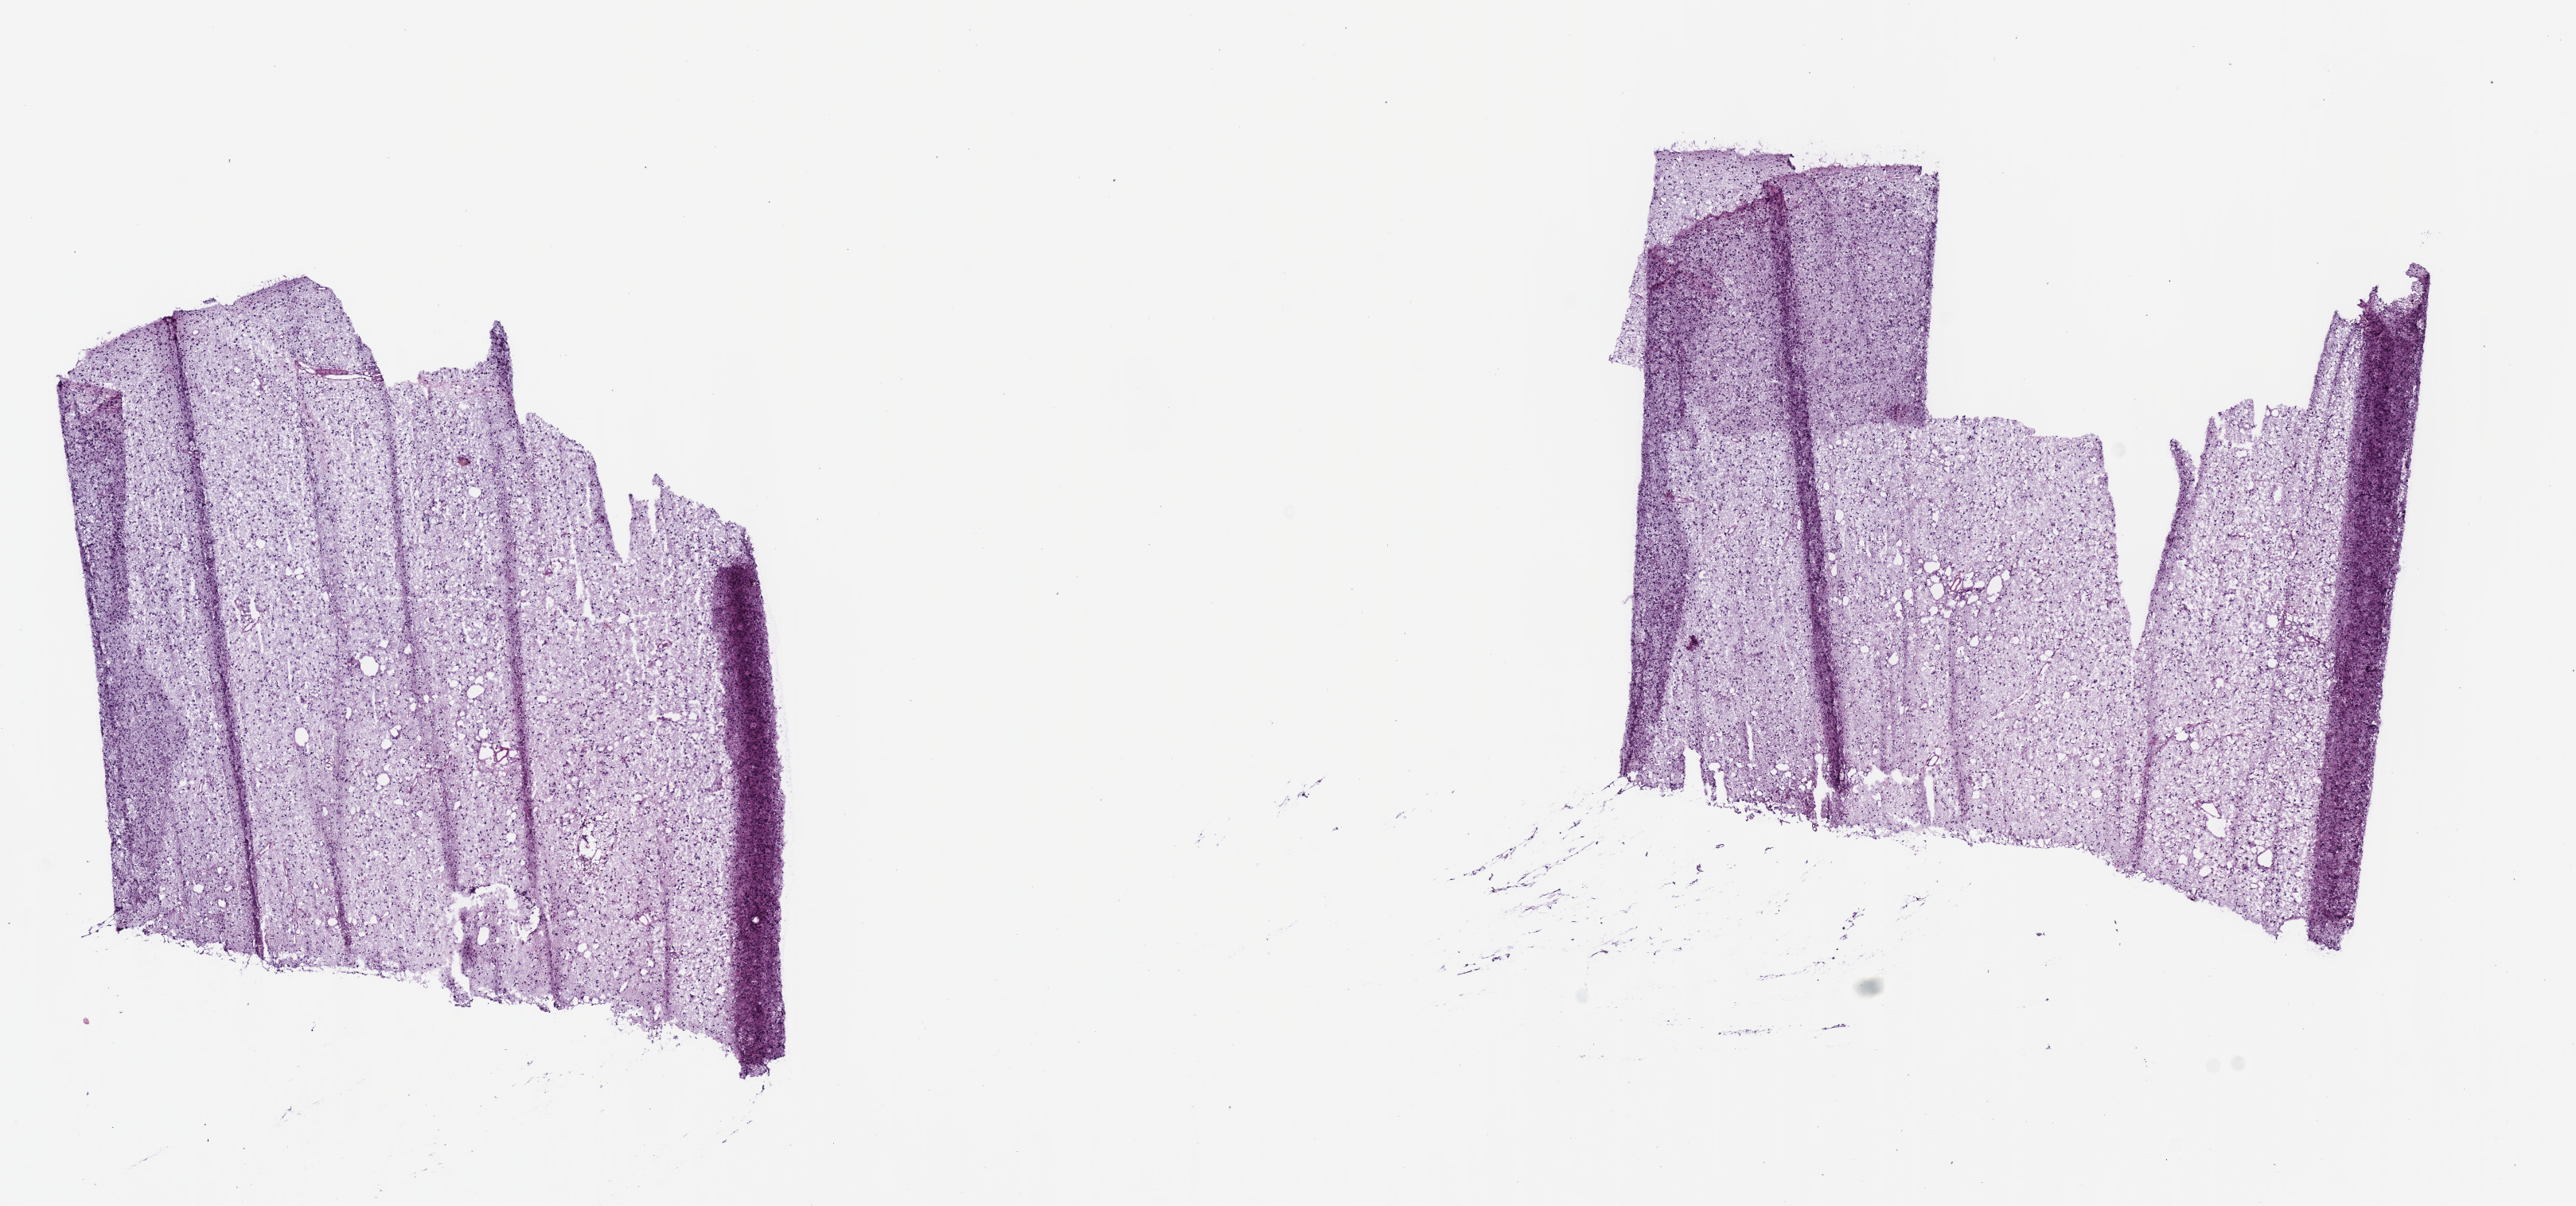
Whole-slide histology image, H&E-stained — whole scanned area (about 12.7 x 6.0 mm, from a 40x scan) shown as a low-resolution overview, frozen section, primary tumour sample from the brain. Male patient; age at initial diagnosis 48 years. Histologic grade: G3 (poorly differentiated). Slide review estimates, as recorded: tumour cells 100%, tumour nuclei 70%, normal cells 0%, stromal cells 0%, necrosis 0%.
* histologic diagnosis: Astrocytoma, anaplastic (cerebrum)
* laterality: left